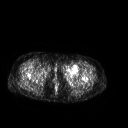
FDG PET of an extremity soft-tissue mass (from a PET/CT study), one axial slice. Position 254 of 267 along the scan axis. 3.27 mm slice thickness. 128 × 128 image matrix. Female patient, age 42 years. From the clinical record (not read from this slice): histological type: pleiomorphic leiomyosarcoma; grade: intermediate; site of the primary tumour: left thigh.
Annotated regions visible in this slice (expert contour drawn on MRI and transferred to this co-registered scan by the dataset authors):
- gross tumour volume including surrounding oedema: bounding box [x1, y1, x2, y2] px = [61, 64, 79, 78]
- gross tumour volume (mass): [62, 64, 79, 78]